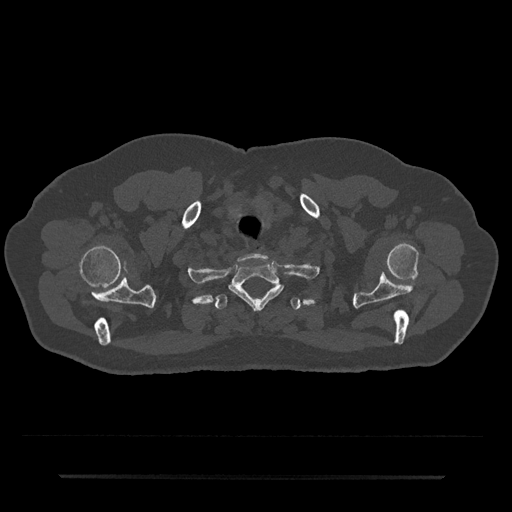
CT including the spine, one axial slice. Slice 635 of 797 in the series (ordered by position). Bone window (W 1800 / L 400 HU). 512 × 512 image matrix. Male patient, age 69 years. From the clinical record (not read from this slice): primary cancer: prostate.
Annotated regions visible in this slice (semi-automatic segmentation, software-assisted and operator-edited):
- T1 vertebra: bounding box <230,261,283,309> (left, top, right, bottom; pixels)
- T2 vertebra: <214,287,300,310>